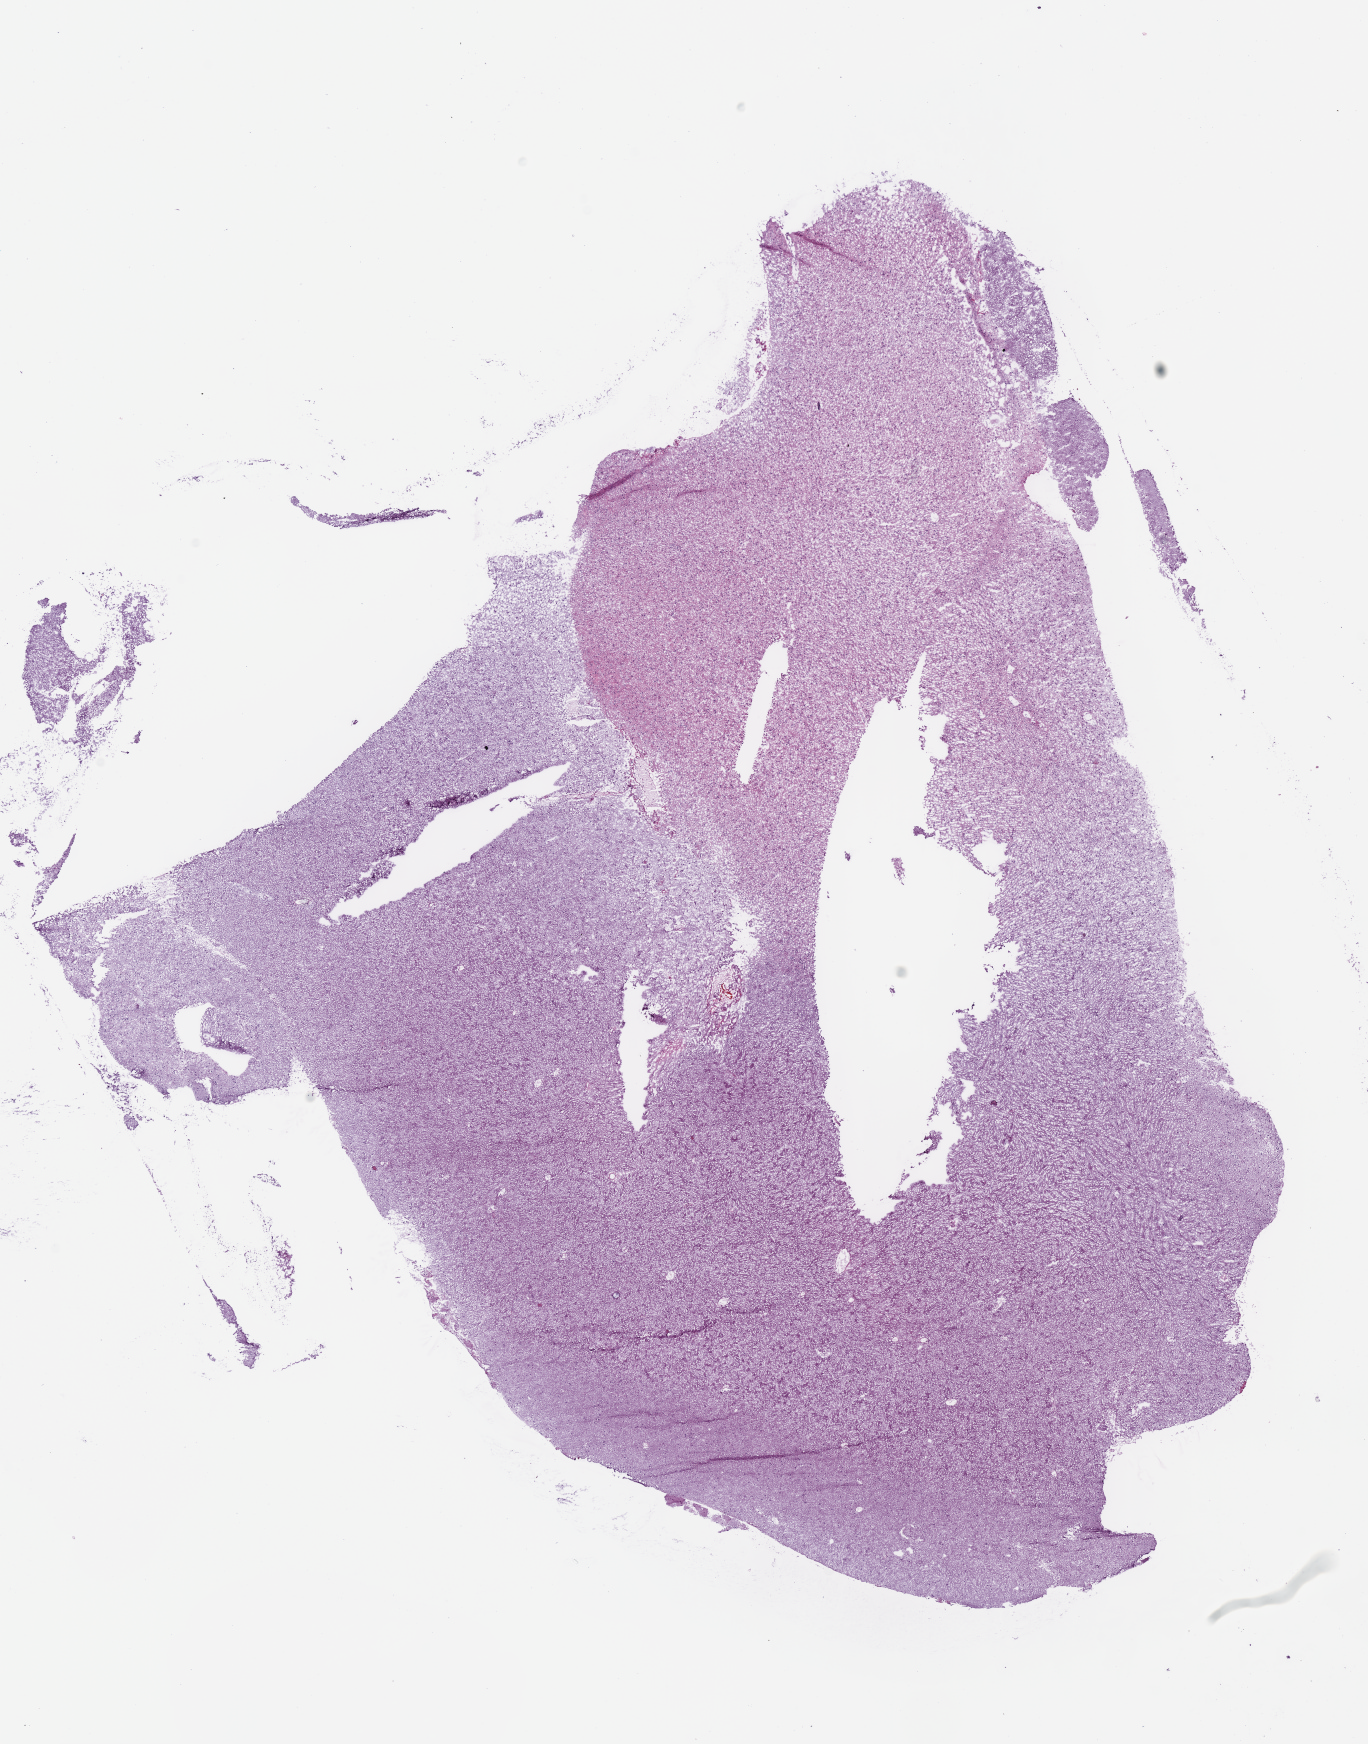
H&E-stained whole-slide image — a low-resolution overview of the entire scanned area, about 10.8 x 13.7 mm, frozen section, sample: primary tumour, brain. Male patient; age at initial diagnosis 29 years. Histologic grade: G2 (moderately differentiated). Slide review estimates, as recorded: tumour cells 80%, tumour nuclei 60%, normal cells 20%, stromal cells 0%, necrosis 0%.
Pathologic diagnosis: Oligodendroglioma, NOS.